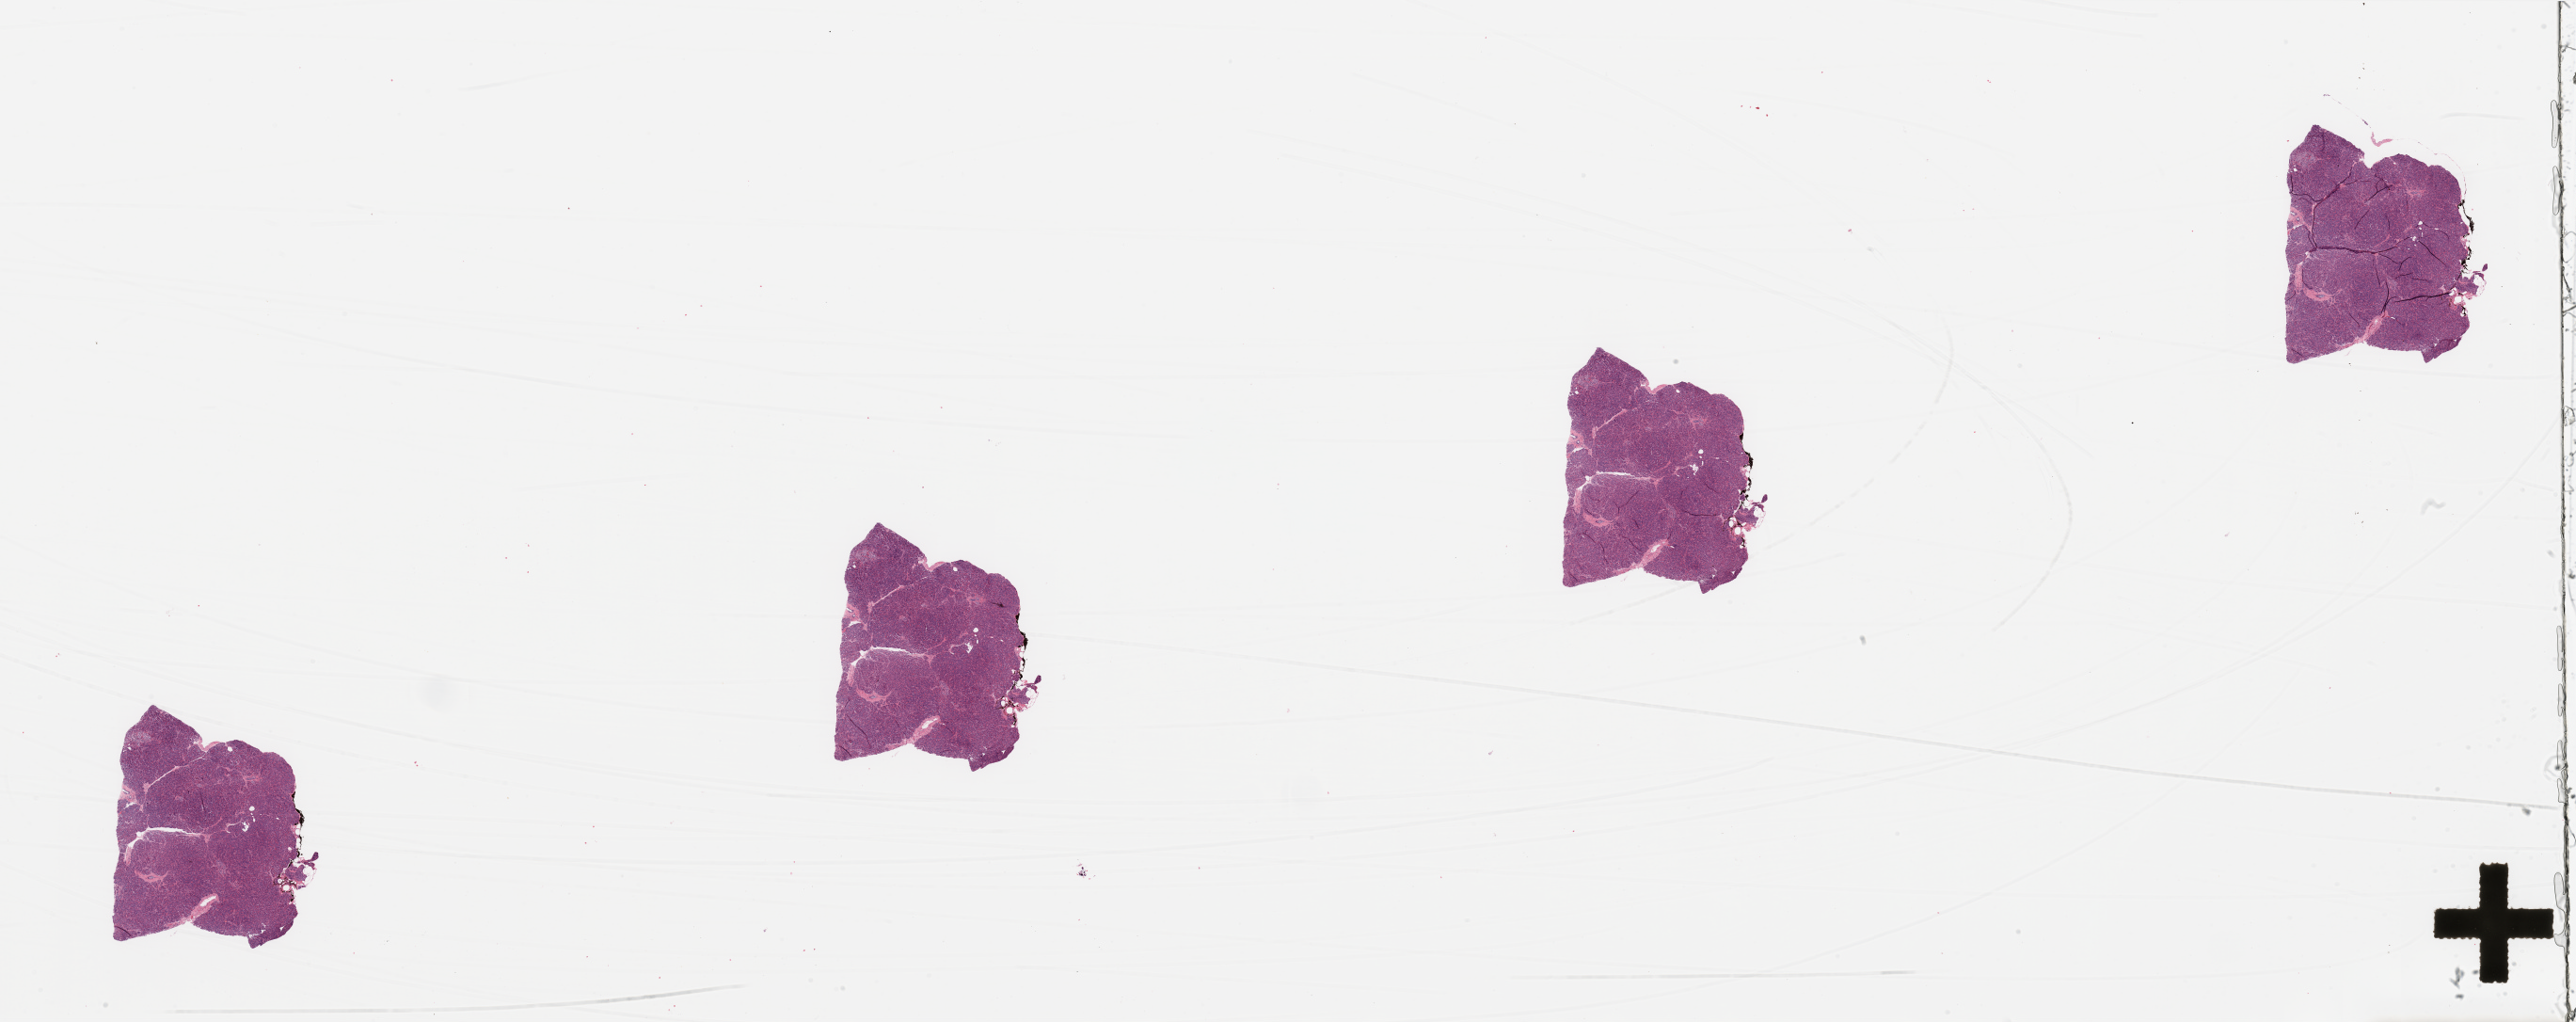
Whole-slide histology image, H&E — a low-resolution overview of the entire scanned area, about 43.3 x 17.2 mm. Normal (non-tumour) tissue sample, pancreas. 63-year-old male patient.
• this section: normal (non-tumour) tissue from the same patient
• patient diagnosis (cohort enrolment): ductal adenocarcinoma (pancreas)